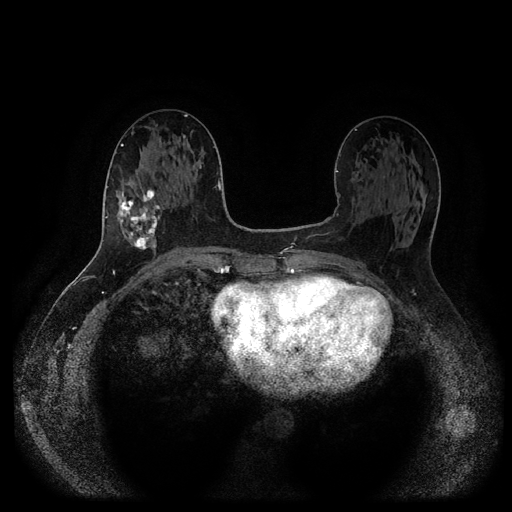
Breast MRI (dynamic contrast-enhanced, multi-phase), one axial slice. Slice 46 of 116 in the series (ordered by position). Dynamic contrast-enhanced series, time point 2 of 5 at this slice position (early post-contrast). 1.5 T. TE 2.6 ms, TR 5.3 ms. 512 × 512 image matrix. Female patient, age 58 years.
Outlined on this slice (semi-automatic segmentation, software-assisted and operator-edited):
- breast lesion (labelled 'tumour' in the annotation; benign lesions carry a separate 'benign' label): box from (x=114, y=186) to (x=162, y=252) px